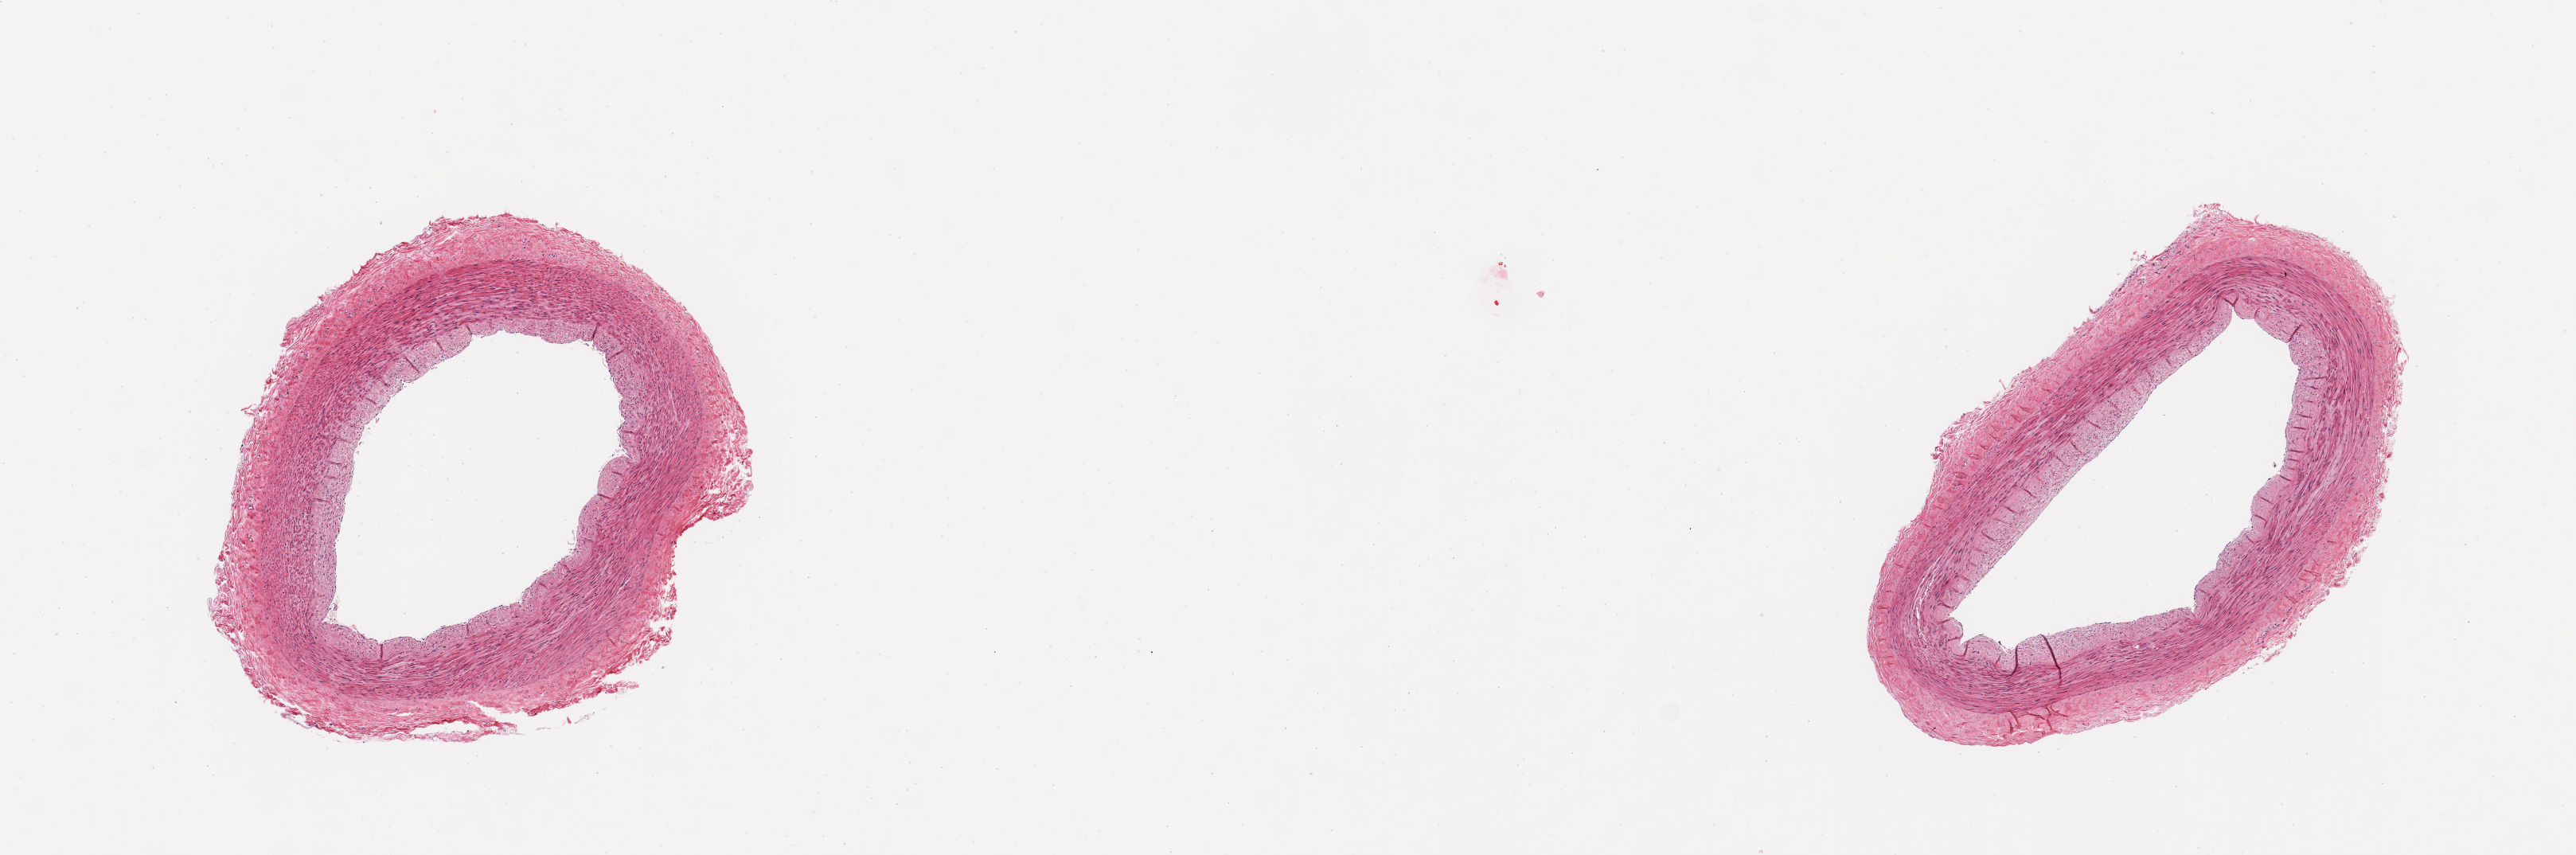
H&E whole-slide image — low-resolution overview of the scanned area, about 12.8 x 4.2 mm. PAXgene-fixed paraffin-embedded (PFPE) section. Target tissue: tibial artery. Donor tissue sample. Donor sex: male.
Pathologist's review note for this sample: 2 pieces, no adherent fat, no atherosis.